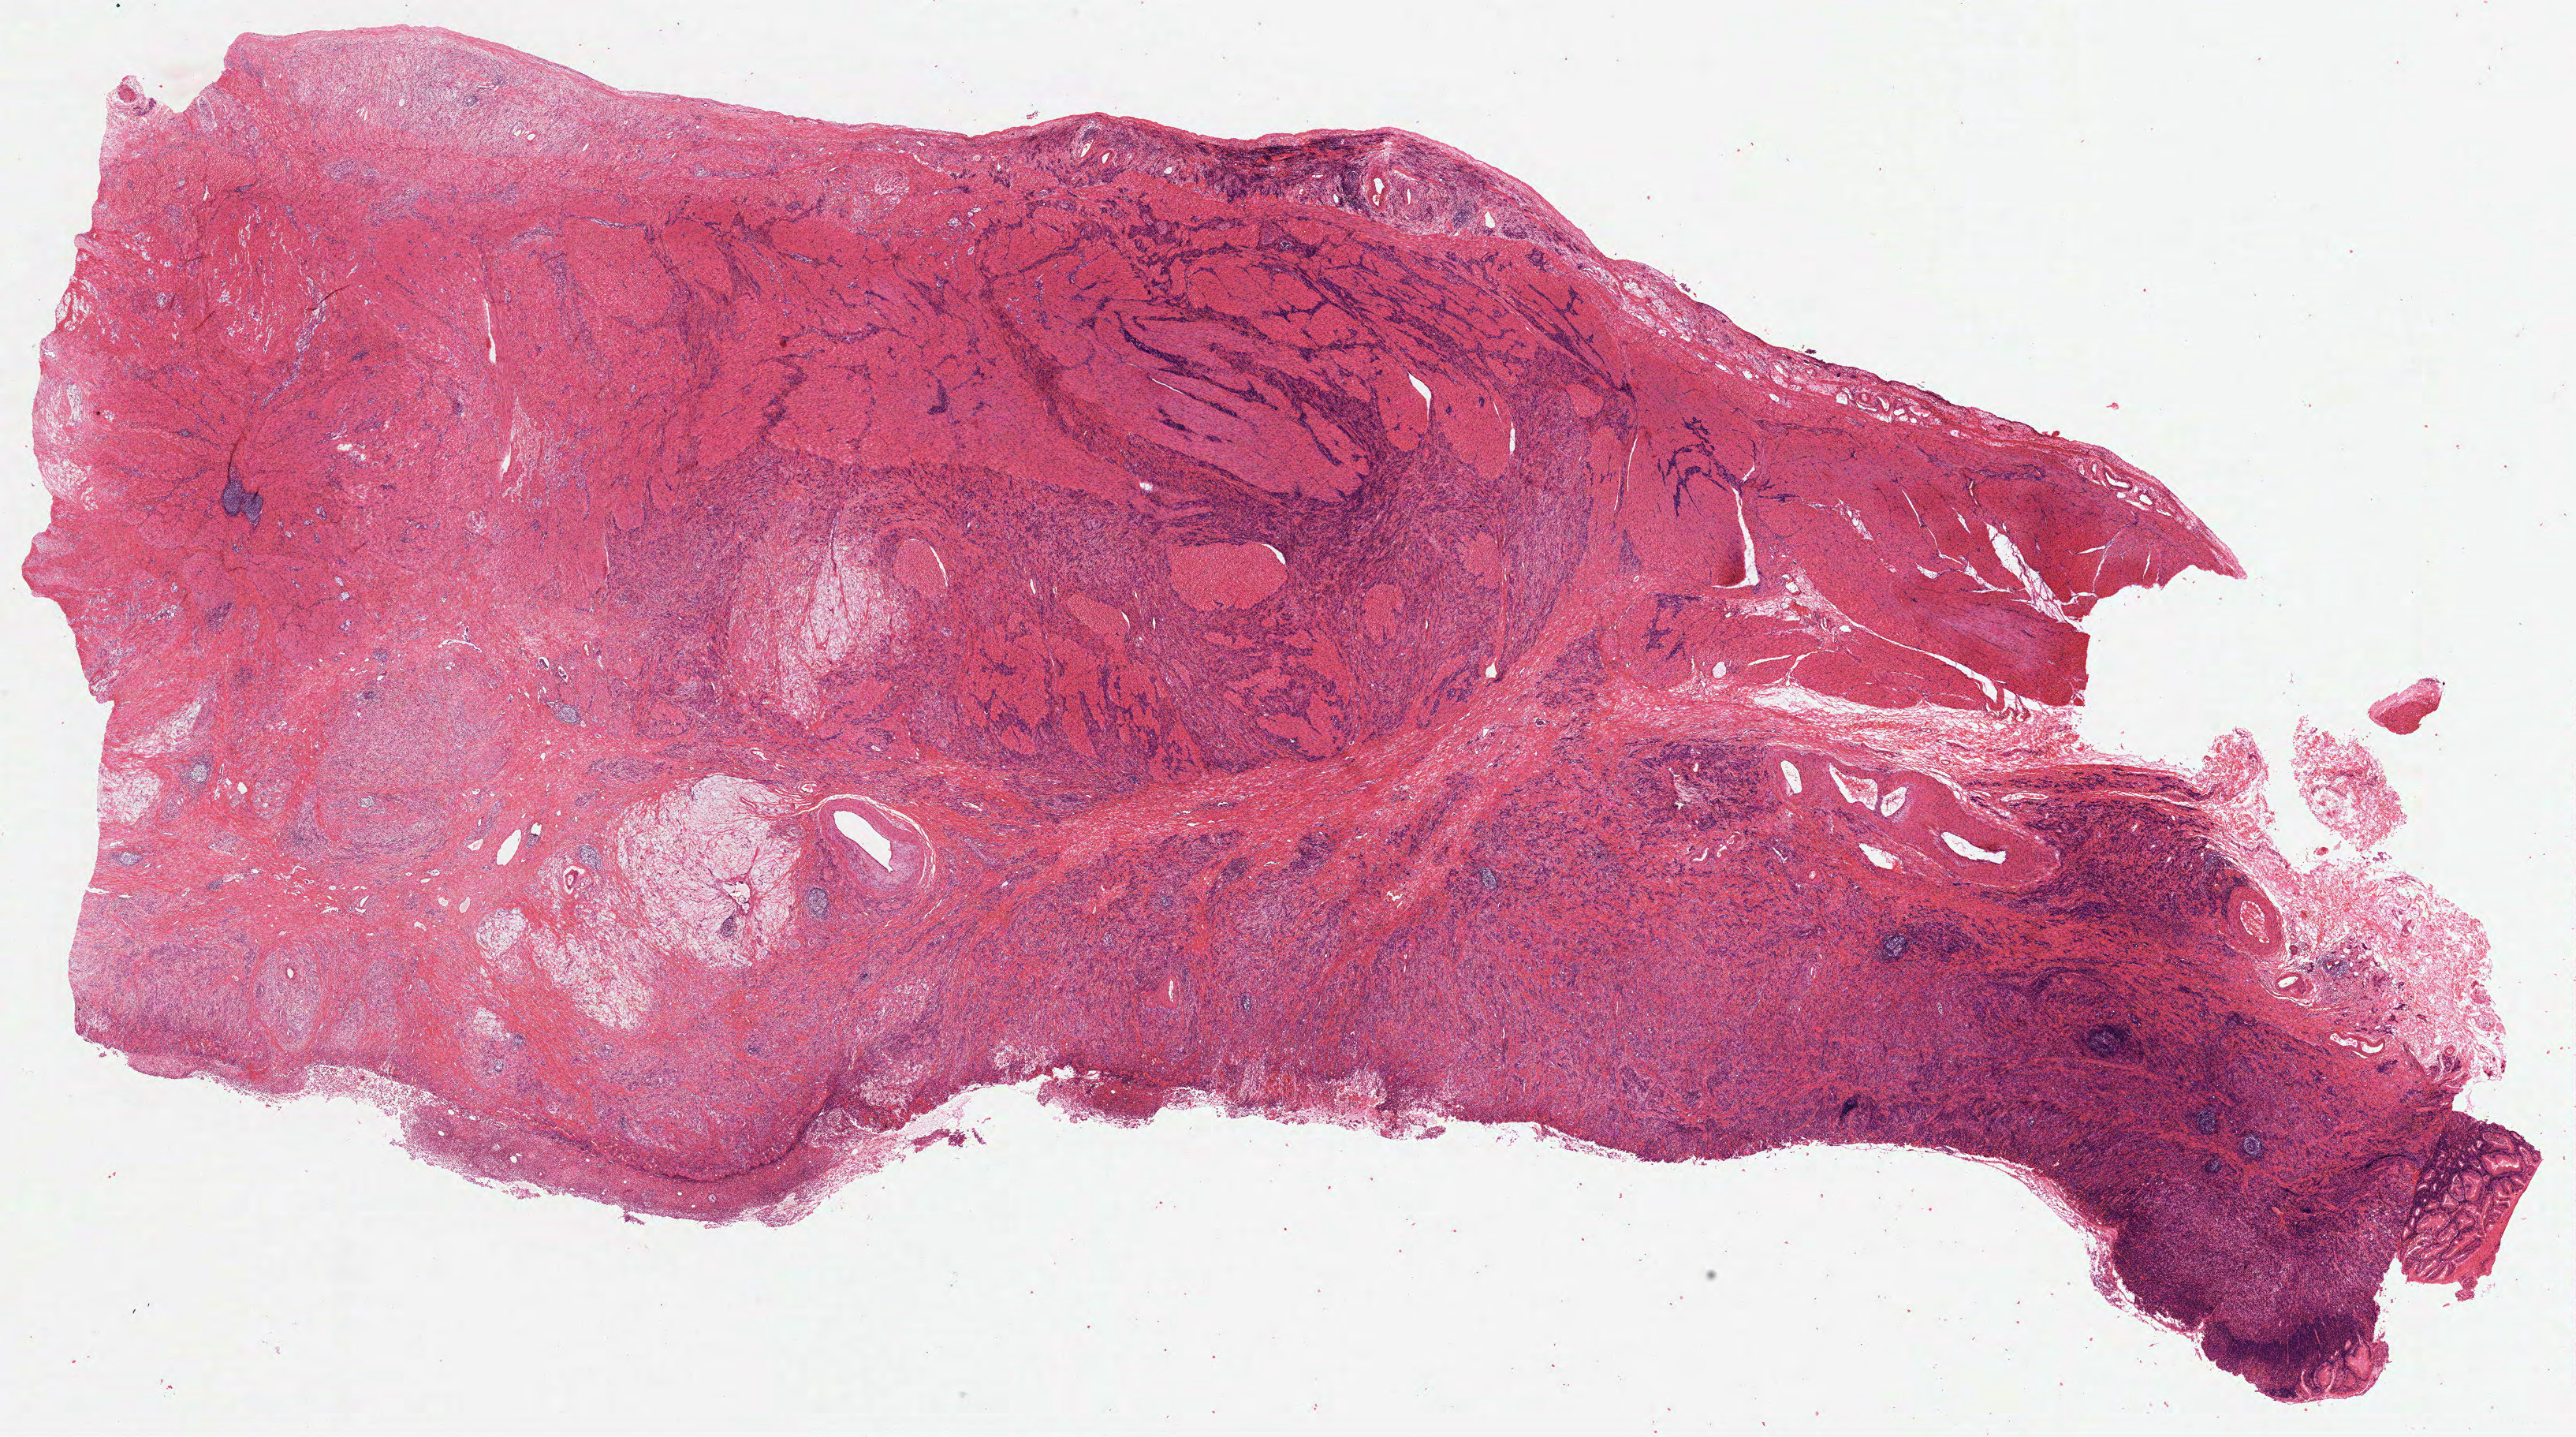
Digitized H&E tissue section (whole slide), a low-resolution overview of the entire scanned area, about 26.3 x 14.7 mm (from a 40x scan); FFPE section; stomach, primary tumour sample. Male, age 55 years at initial diagnosis.
Pathologic diagnosis: Adenocarcinoma, NOS (gastric antrum).